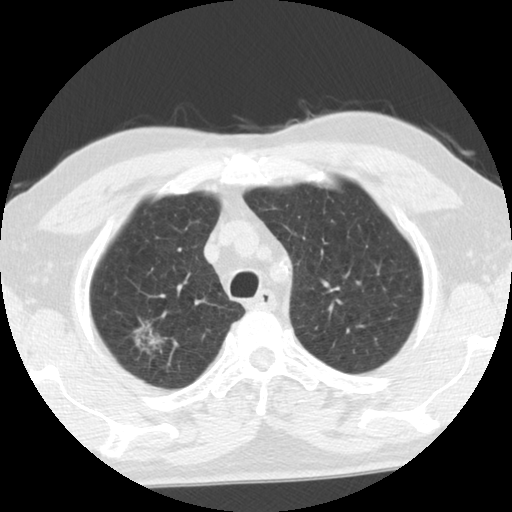
Low-dose screening chest CT, one axial slice. Slice 92 of 116 in the series (ordered by position). Reconstruction kernel STANDARD. Lung window (W 1500 / L -600 HU). 2.5 mm slice thickness. 512 × 512 image matrix, field of view 330 × 330 mm.
Outlined on this slice (outlined manually by an expert reader):
- lesion 1 (tumor, upper lobe of right lung): bounding box [x1, y1, x2, y2] px = [131, 321, 169, 355]